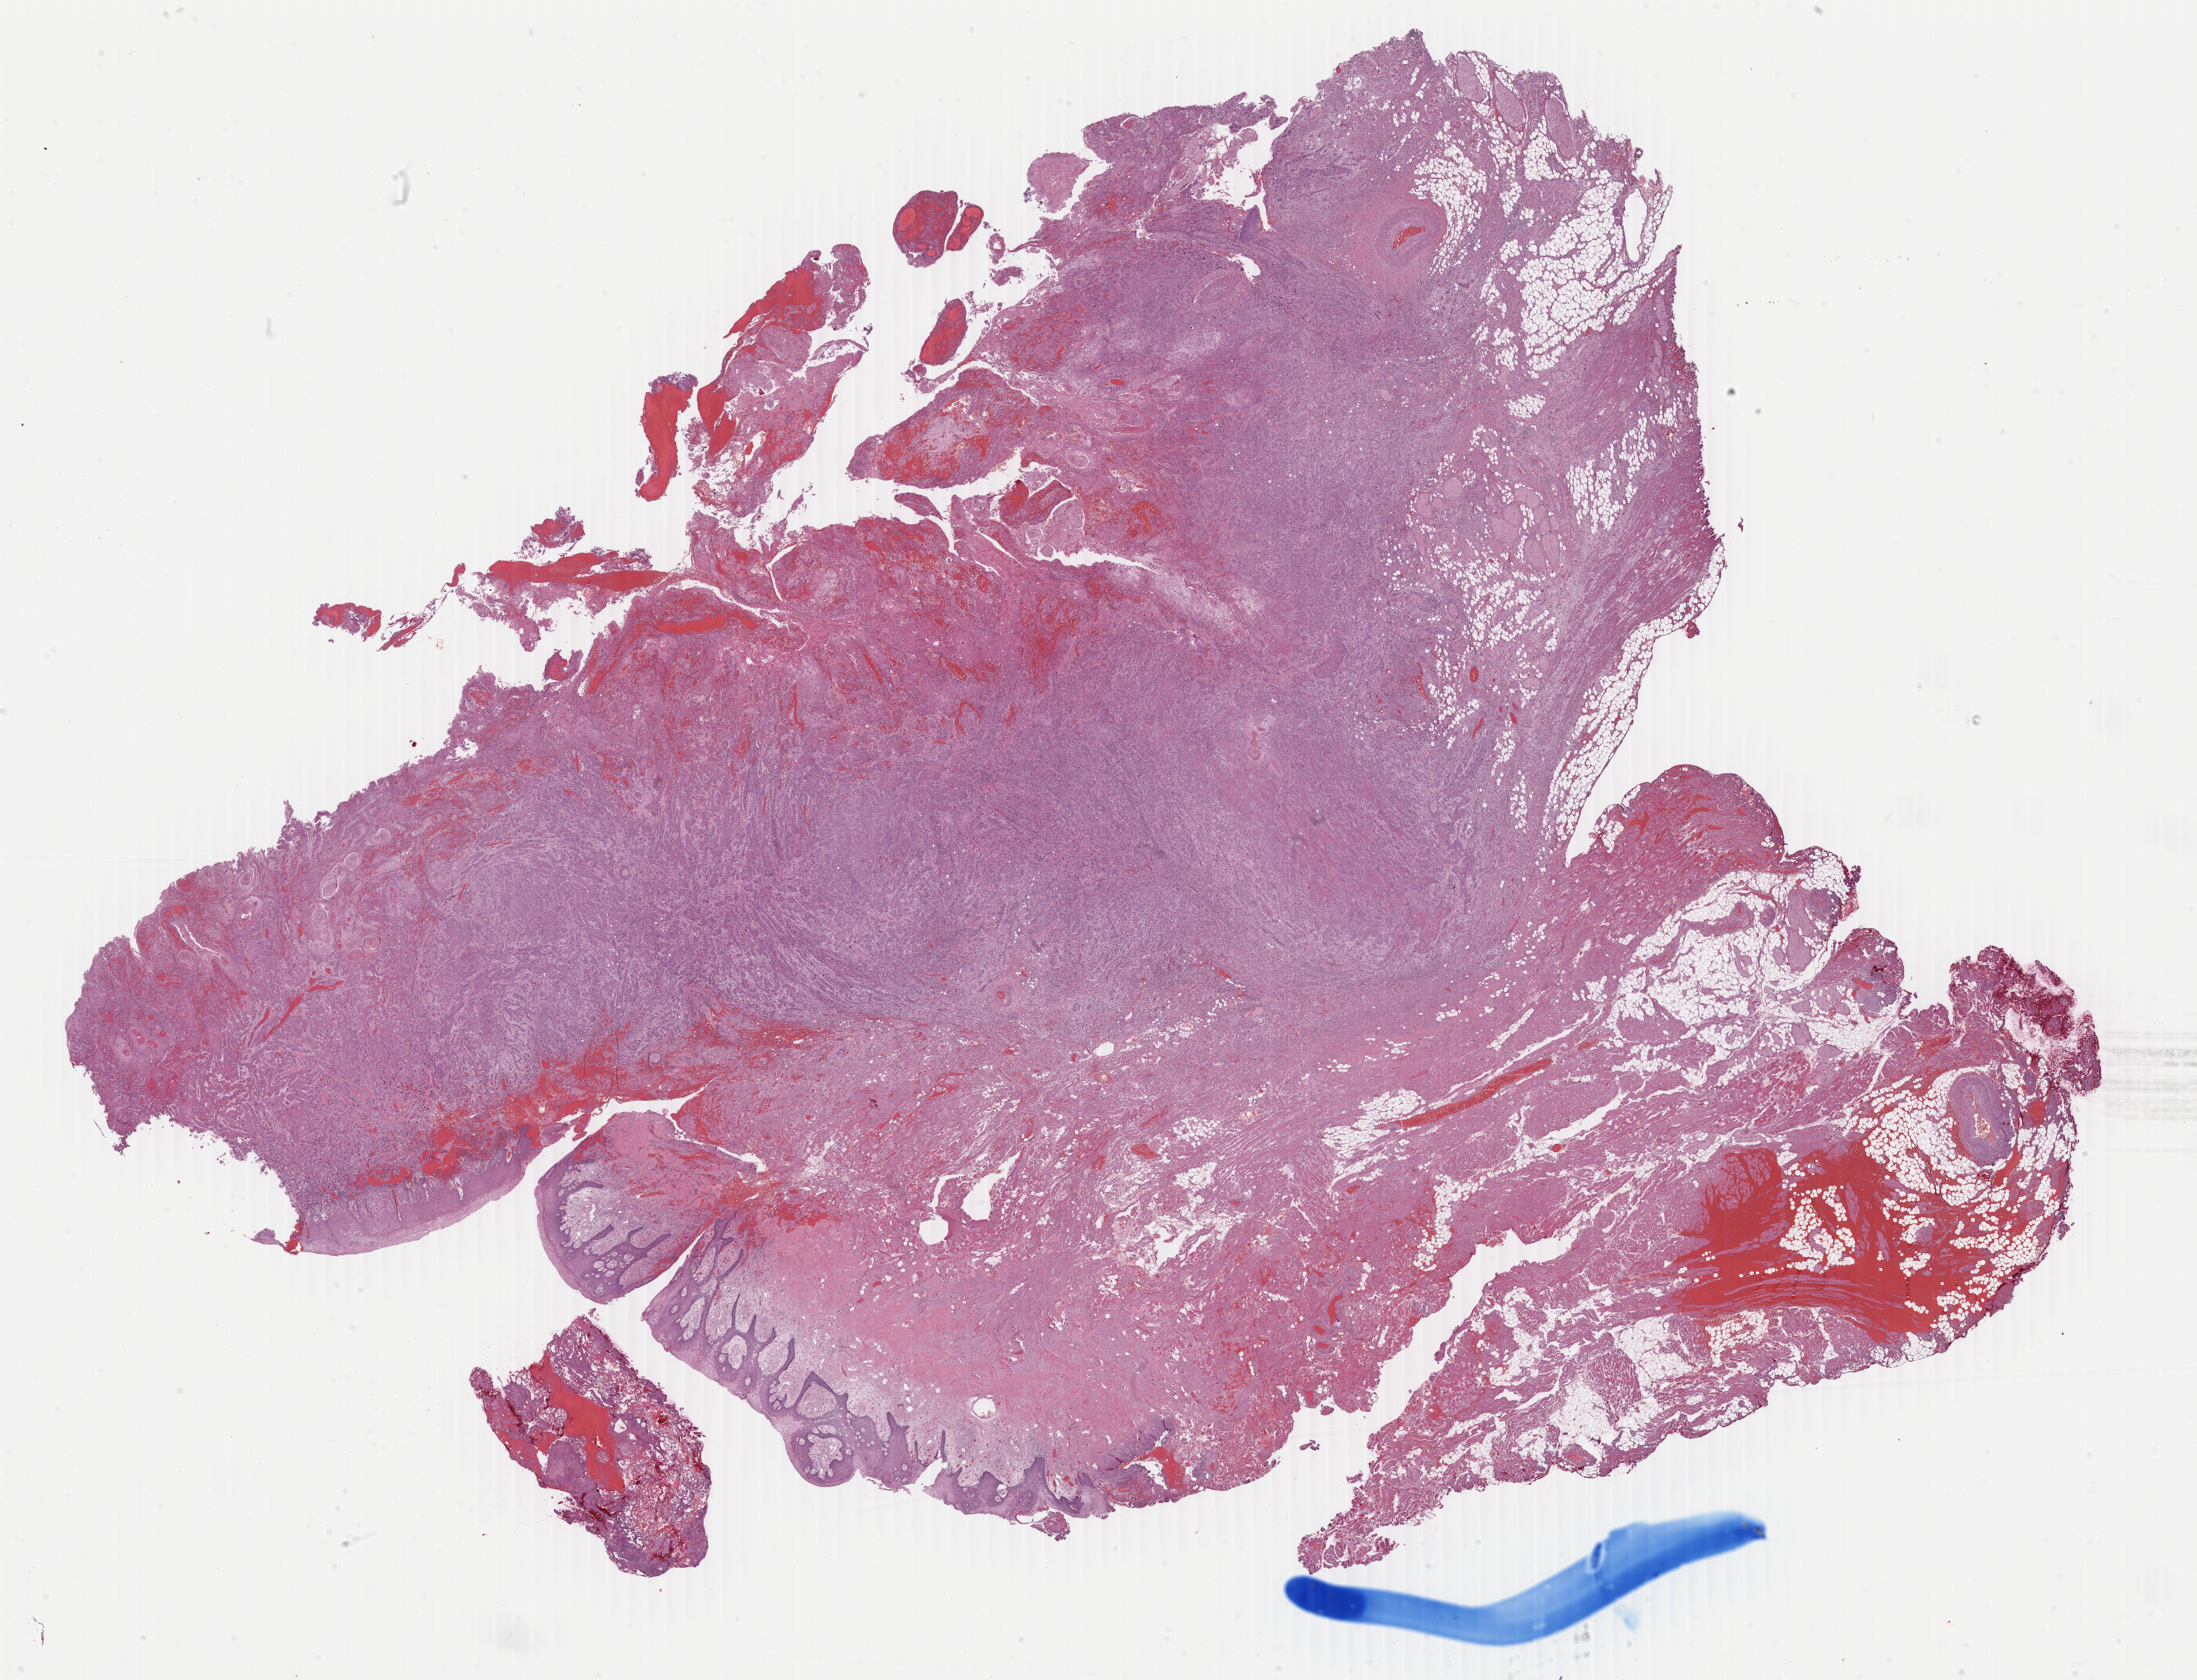
Whole-slide histology image, H&E-stained — shown as a low-resolution overview of the whole scanned area (about 27.6 x 21.1 mm, from a 40x scan). Formalin-fixed paraffin-embedded (FFPE) diagnostic section. Primary tumour sample from the head and neck. Patient: female, age at initial diagnosis 70 years. Histologic grade: G2 (moderately differentiated).
• TNM: T3 N2b M0
• laterality: right
• pathologic diagnosis: Squamous cell carcinoma, keratinizing, NOS (tongue, NOS)
• AJCC pathologic stage: IVA (7th edition)